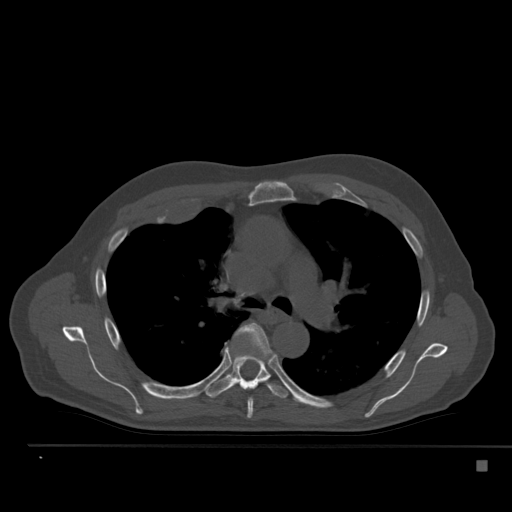
CT including the spine, one axial slice; position 355 of 517 along the scan axis; reconstruction kernel Br40s; bone window (W 1800 / L 400 HU); 512 × 512 image matrix, field of view 408 × 408 mm. Patient: male, 70 years. From the clinical record (not read from this slice): primary cancer: renal.
Outlined on this slice (semi-automatically segmented with operator editing):
- T5 vertebra: bounding box [x1, y1, x2, y2] px = [239, 323, 272, 418]
- T6 vertebra: [206, 346, 292, 398]